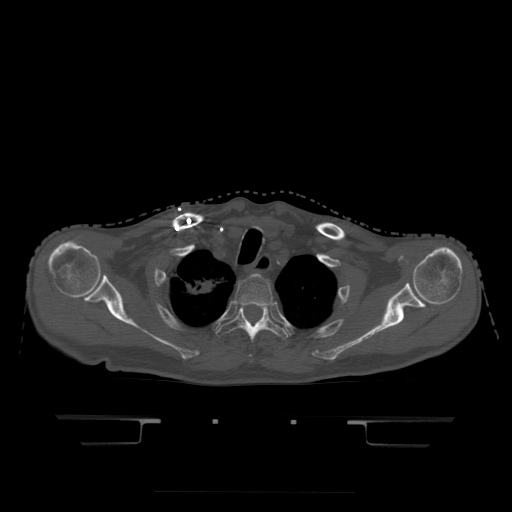
CT including the spine, one axial slice. Slice 377 of 522 in the series (ordered by position). Bone window (W 1800 / L 400 HU). 1.25 mm slice thickness. 512 × 512 image matrix, field of view 436 × 436 mm. Patient age 68 years. From the clinical record (not read from this slice): primary cancer: urothelial.
Structures marked on this image (semi-automatic segmentation, software-assisted and operator-edited):
- T2 vertebra: bounding box (x1, y1, x2, y2) in pixels: (235, 274, 273, 306)
- T3 vertebra: (217, 304, 288, 345)